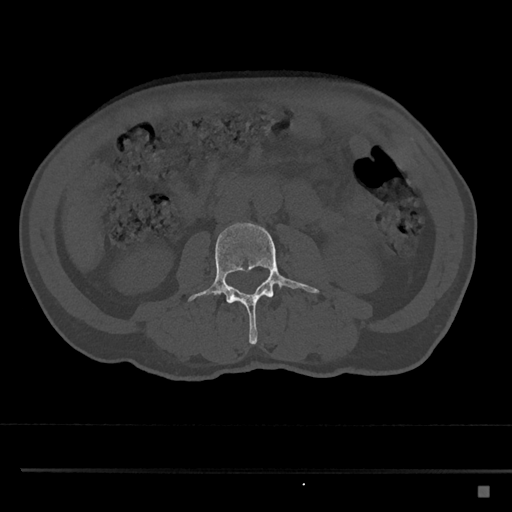
CT including the spine, one axial slice. Position 696 of 797 along the scan axis. Reconstruction kernel Br40s/3. Bone window (W 1800 / L 400 HU). 0.5 mm slice thickness. 512 × 512 image matrix, field of view 391 × 391 mm. Male patient, age 59 years. From the clinical record (not read from this slice): primary cancer: prostate.
Annotated regions visible in this slice (semi-automatically segmented with operator editing):
- L3 vertebra: bounding box (x1, y1, x2, y2) in pixels: (188, 223, 319, 345)